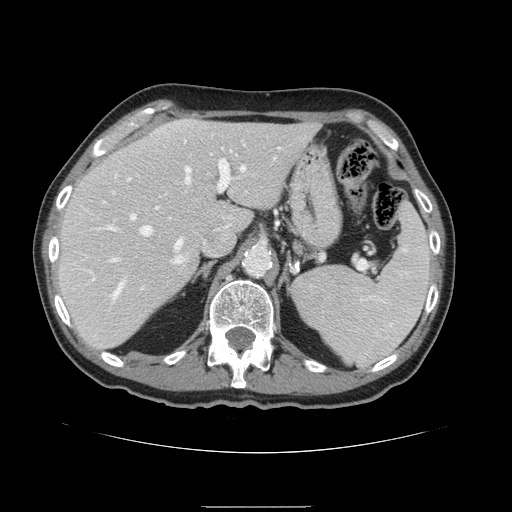
Contrast-enhanced abdominal CT, one axial slice. Slice 104 of 168 in the series (ordered by position). 120 kVp. Soft-tissue window (W 400 / L 40 HU). 2.5 mm slice thickness. 512 × 512 image matrix, field of view 386 × 386 mm. Male patient, age 74 years. Case-level facts recorded for this patient, not image findings: diagnosis: colorectal cancer liver metastases, imaged before liver resection; multiple liver metastases: no; largest metastasis: 14.5 cm; chemotherapy before resection: no.
Structures marked on this image (outlined manually by an expert reader):
- hepatic veins: bounding box (x1, y1, x2, y2) in pixels: (109, 166, 246, 297)
- liver: (57, 119, 320, 350)
- planned liver remnant (the part of the liver to remain after resection): (57, 119, 320, 349)
- portal vein (with intrahepatic branches): (101, 159, 230, 248)